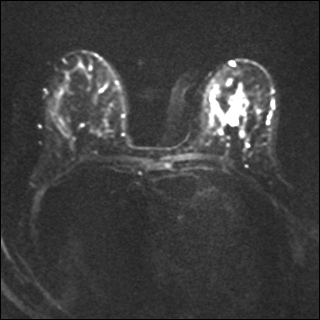
Breast MRI, one axial slice; position 21 of 40 along the scan axis; diffusion-weighted series; image 2 of 4 stored at this slice position (different b-values; order by instance number); 1.5 T; 4 mm slice thickness; 320 × 320 image matrix, field of view 320 × 320 mm. Female patient.
Annotated regions visible in this slice (manually delineated by an expert):
- tumour on diffusion-weighted imaging: bounding box [x1, y1, x2, y2] px = [228, 103, 242, 124]